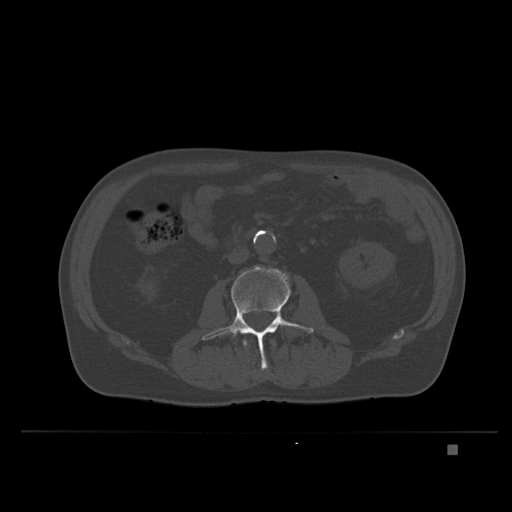
CT including the spine, one axial slice; position 98 of 435 along the scan axis; bone window (W 1800 / L 400 HU); 1.5 mm slice thickness; 512 × 512 image matrix. Patient: male, 73 years. Case-level facts recorded for this patient, not image findings: primary cancer: skin.
Annotated regions visible in this slice (semi-automatic segmentation, software-assisted and operator-edited):
- L2 vertebra: bounding box [x1, y1, x2, y2] px = [243, 340, 276, 378]
- L3 vertebra: [202, 265, 314, 369]